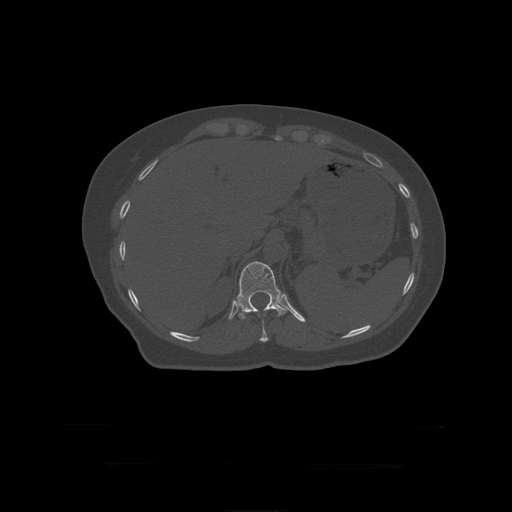
CT including the spine, one axial slice; position 205 of 399 along the scan axis; reconstruction kernel STANDARD; 120 kVp; bone window (W 1800 / L 400 HU); 1.25 mm slice thickness; 512 × 512 image matrix, field of view 450 × 450 mm. Patient age 41 years. From the clinical record (not read from this slice): primary cancer: breast.
Annotated regions visible in this slice (semi-automatic segmentation, software-assisted and operator-edited):
- T11 vertebra: bounding box [x1, y1, x2, y2] px = [258, 315, 269, 342]
- T12 vertebra: [237, 262, 290, 319]